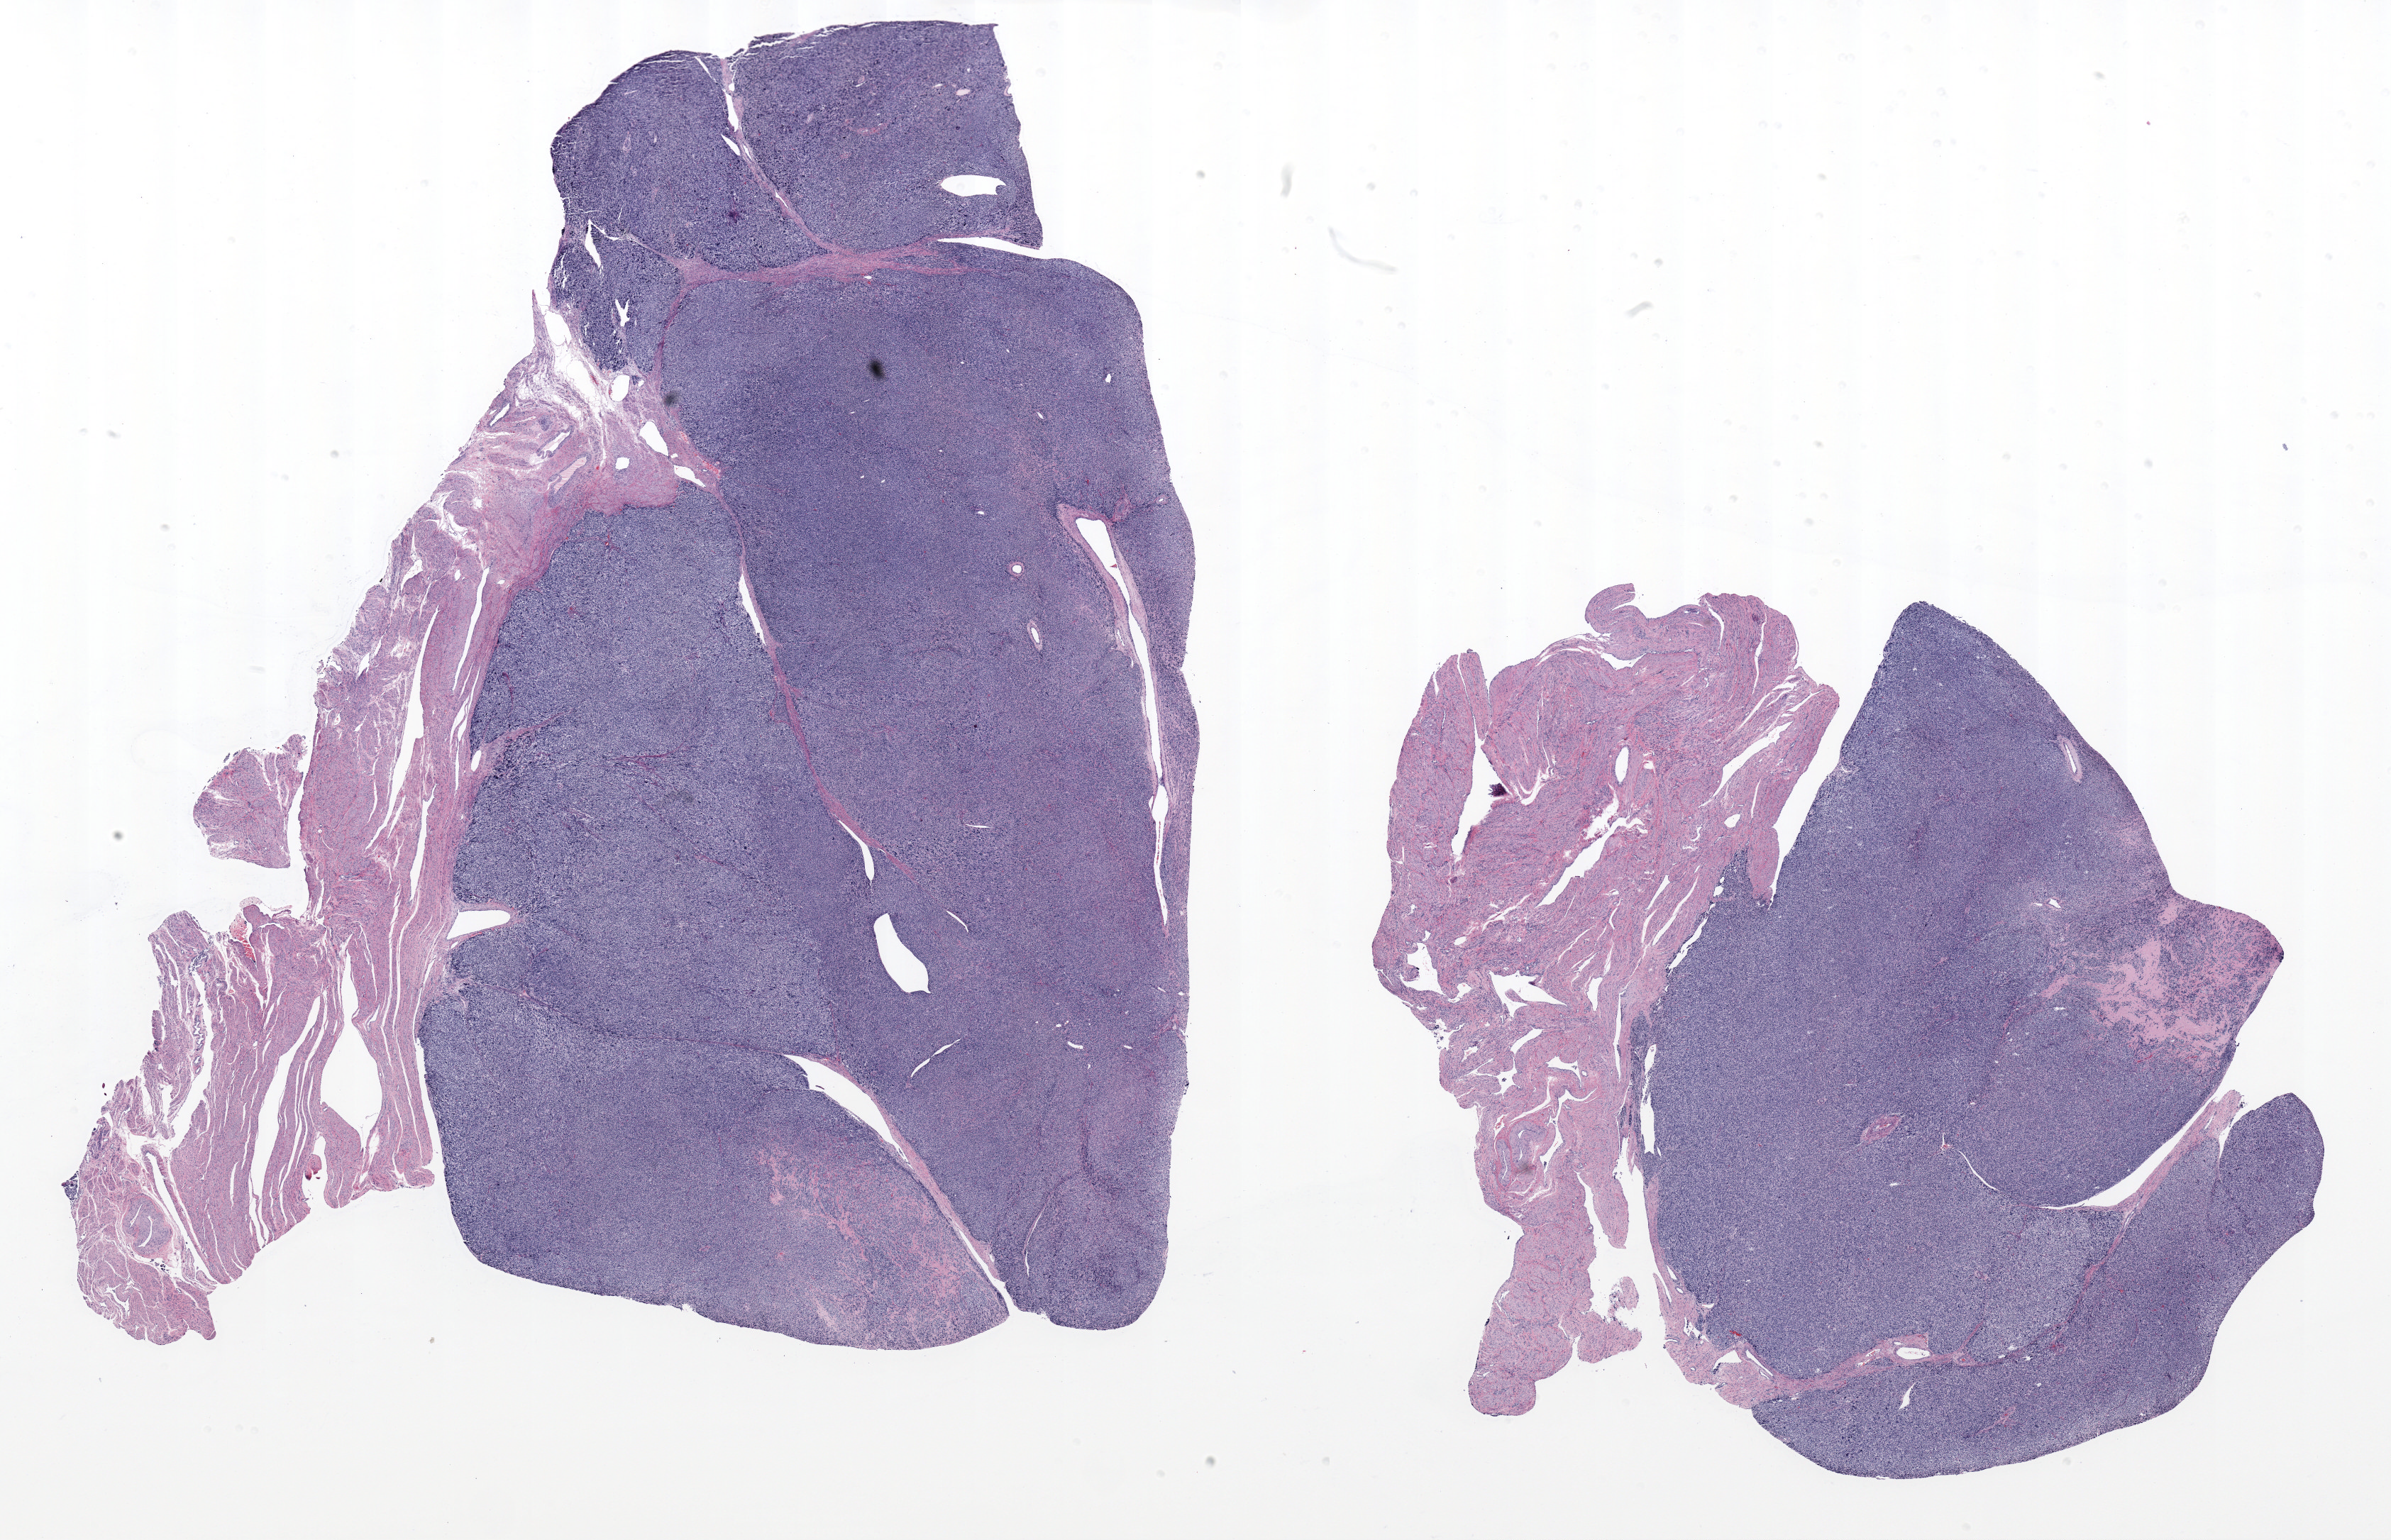
H&E-stained whole-slide image, whole scanned area (about 26.9 x 17.3 mm) shown as a low-resolution overview, formalin-fixed paraffin-embedded (FFPE) diagnostic section, uterus, primary tumour sample. Female patient; age at initial diagnosis 55 years.
* diagnosis: Leiomyosarcoma, NOS